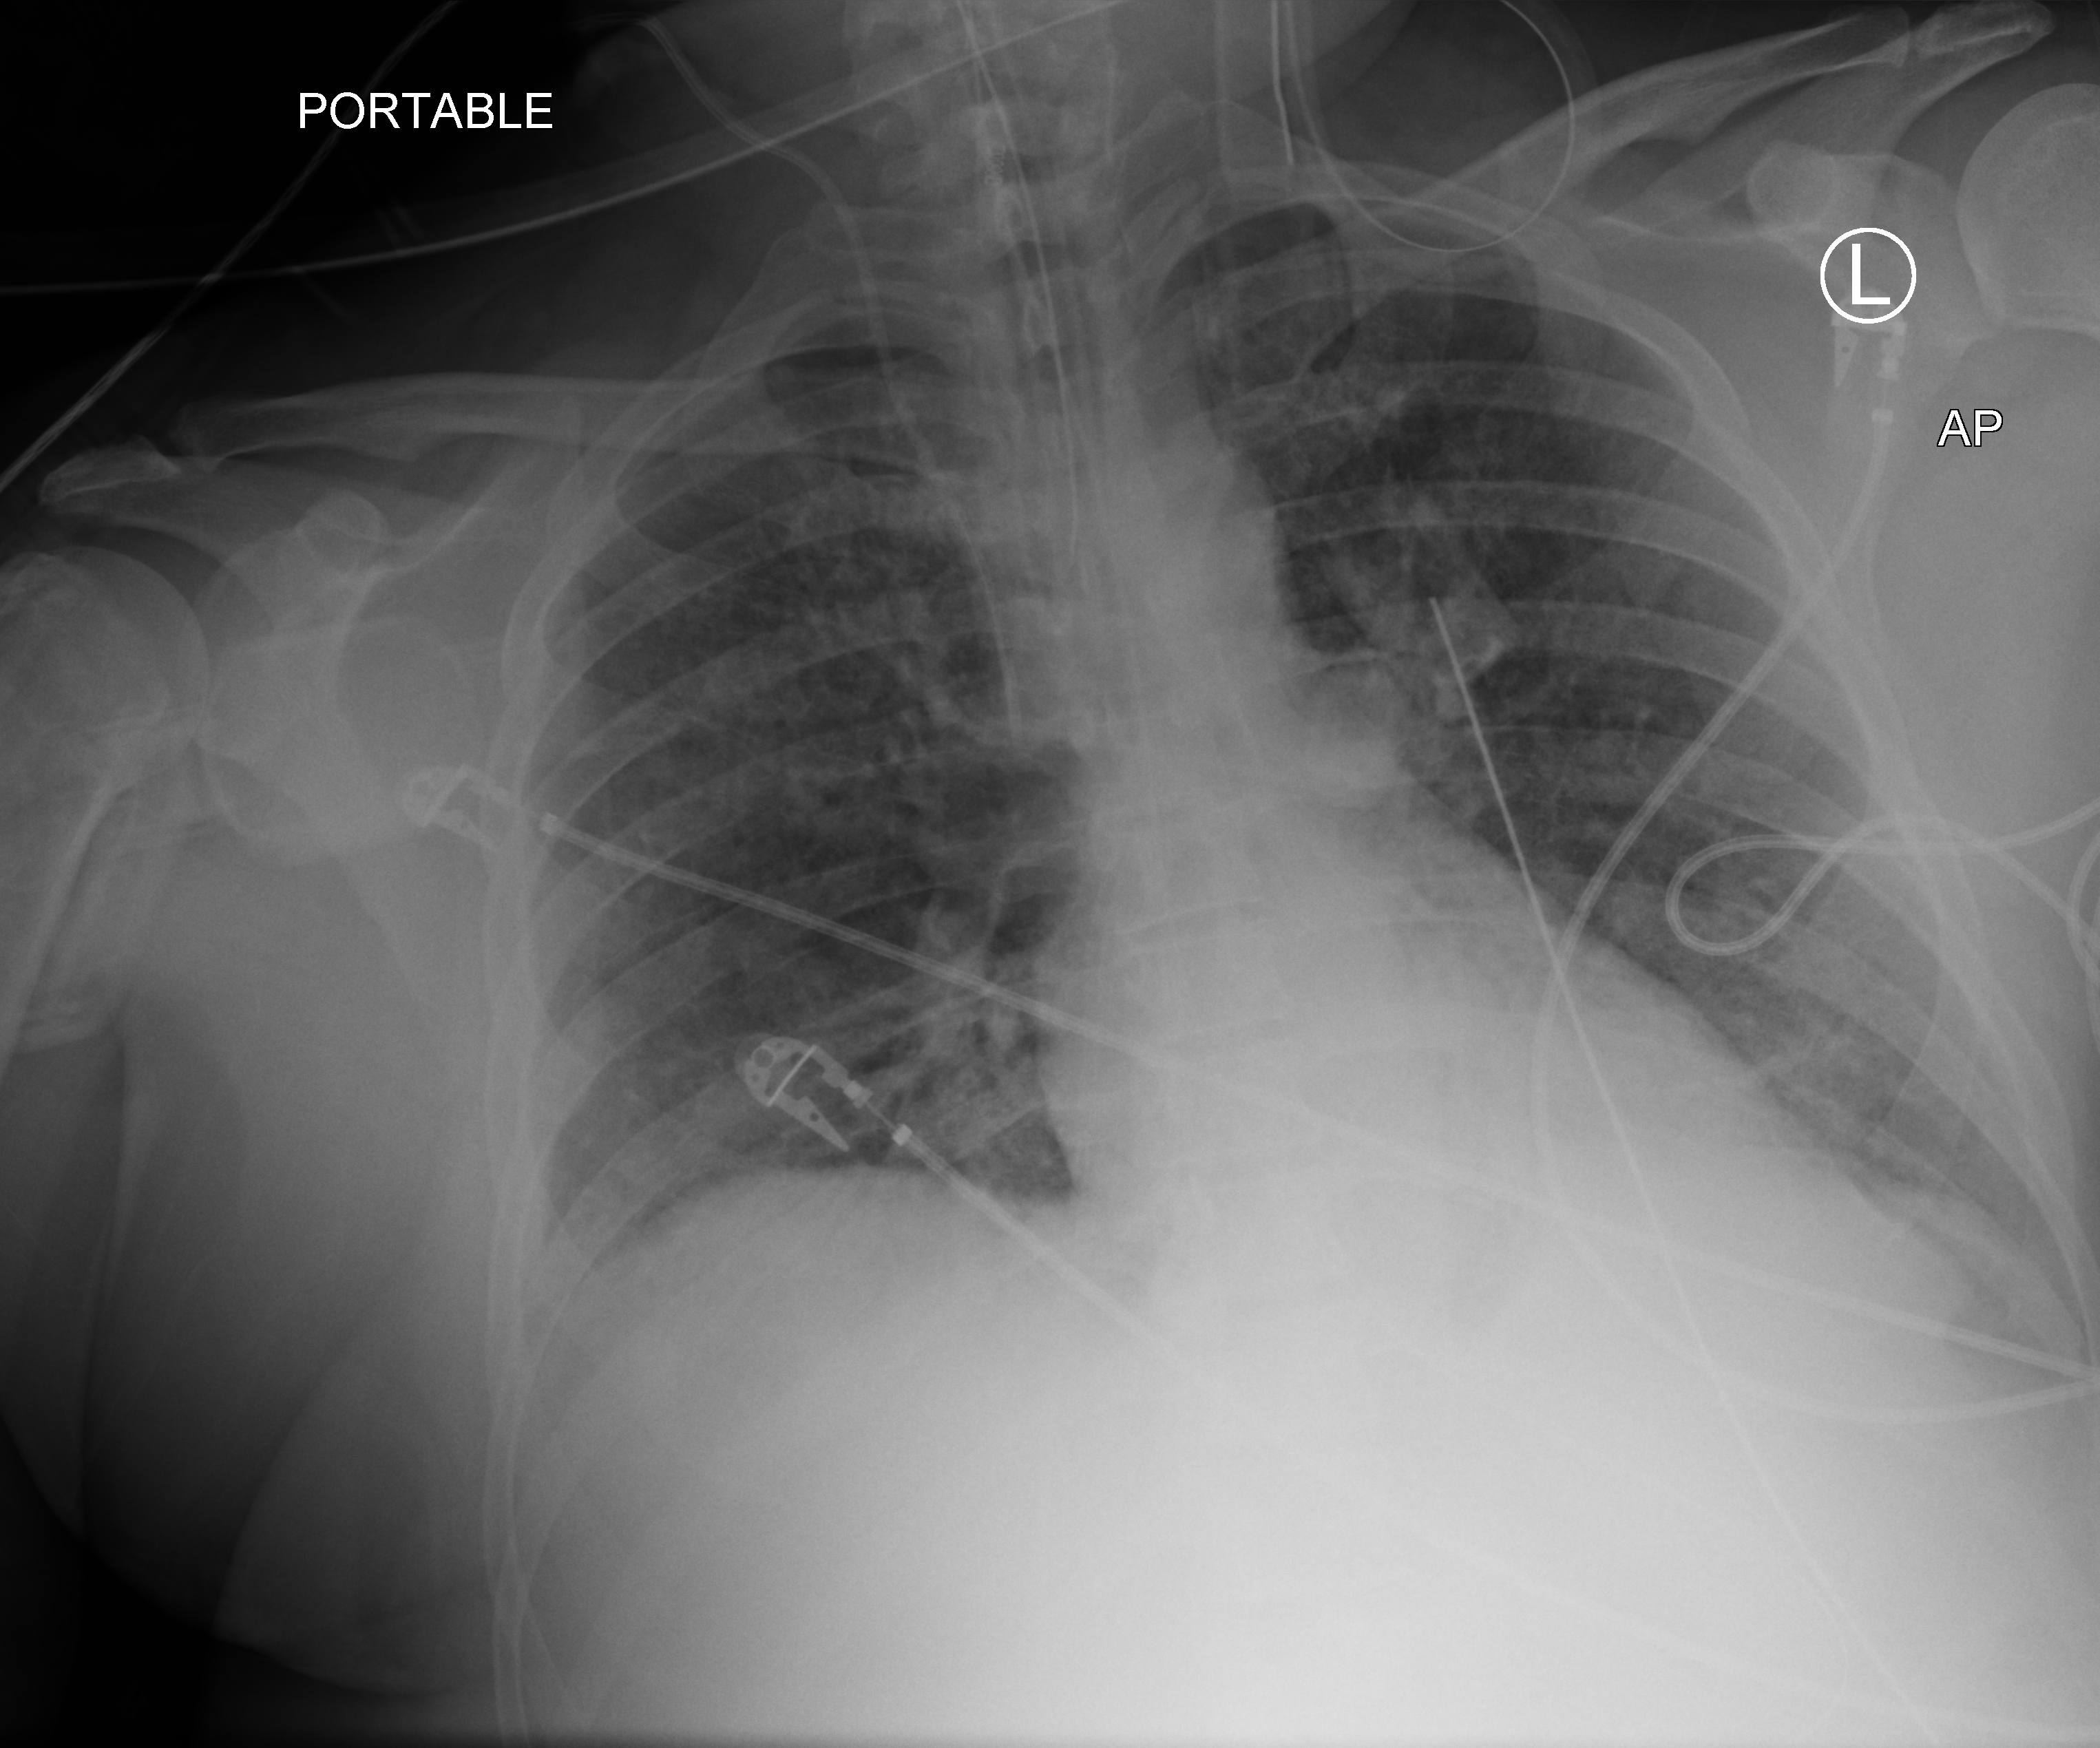
Bedside chest radiograph (computed radiography); anteroposterior (AP) projection. Male patient hospitalised with COVID-19, age 18–59 years.
Admission-level facts for this patient (not findings on this image; timing relative to this image not recorded): length of hospital stay: 96 days.